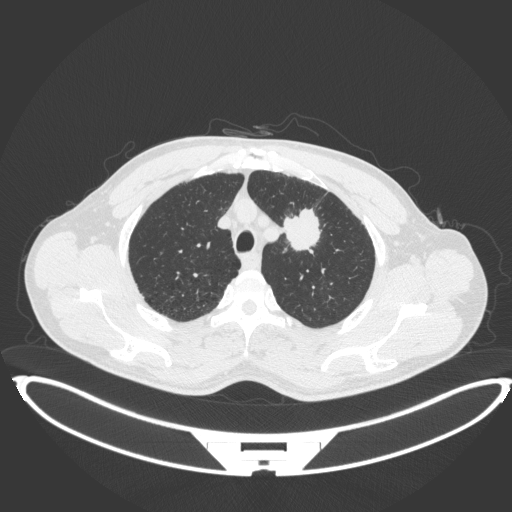
Chest CT, one axial slice. Slice 353 of 407 in the series (ordered by position). Reconstruction kernel B31f. 120 kVp. Lung window (W 1500 / L -600 HU). 1 mm slice thickness. 512 × 512 image matrix. Patient: male, 60 years. From the clinical record (not read from this slice): clinical TNM (as recorded): T2a N0 M0; histopathological grade: G1-G2.
Annotated regions visible in this slice (rectangle marked by the reading radiologist):
- lung tumour (recorded histology: squamous cell carcinoma): bounding box [x1, y1, x2, y2] px = [282, 202, 322, 253]